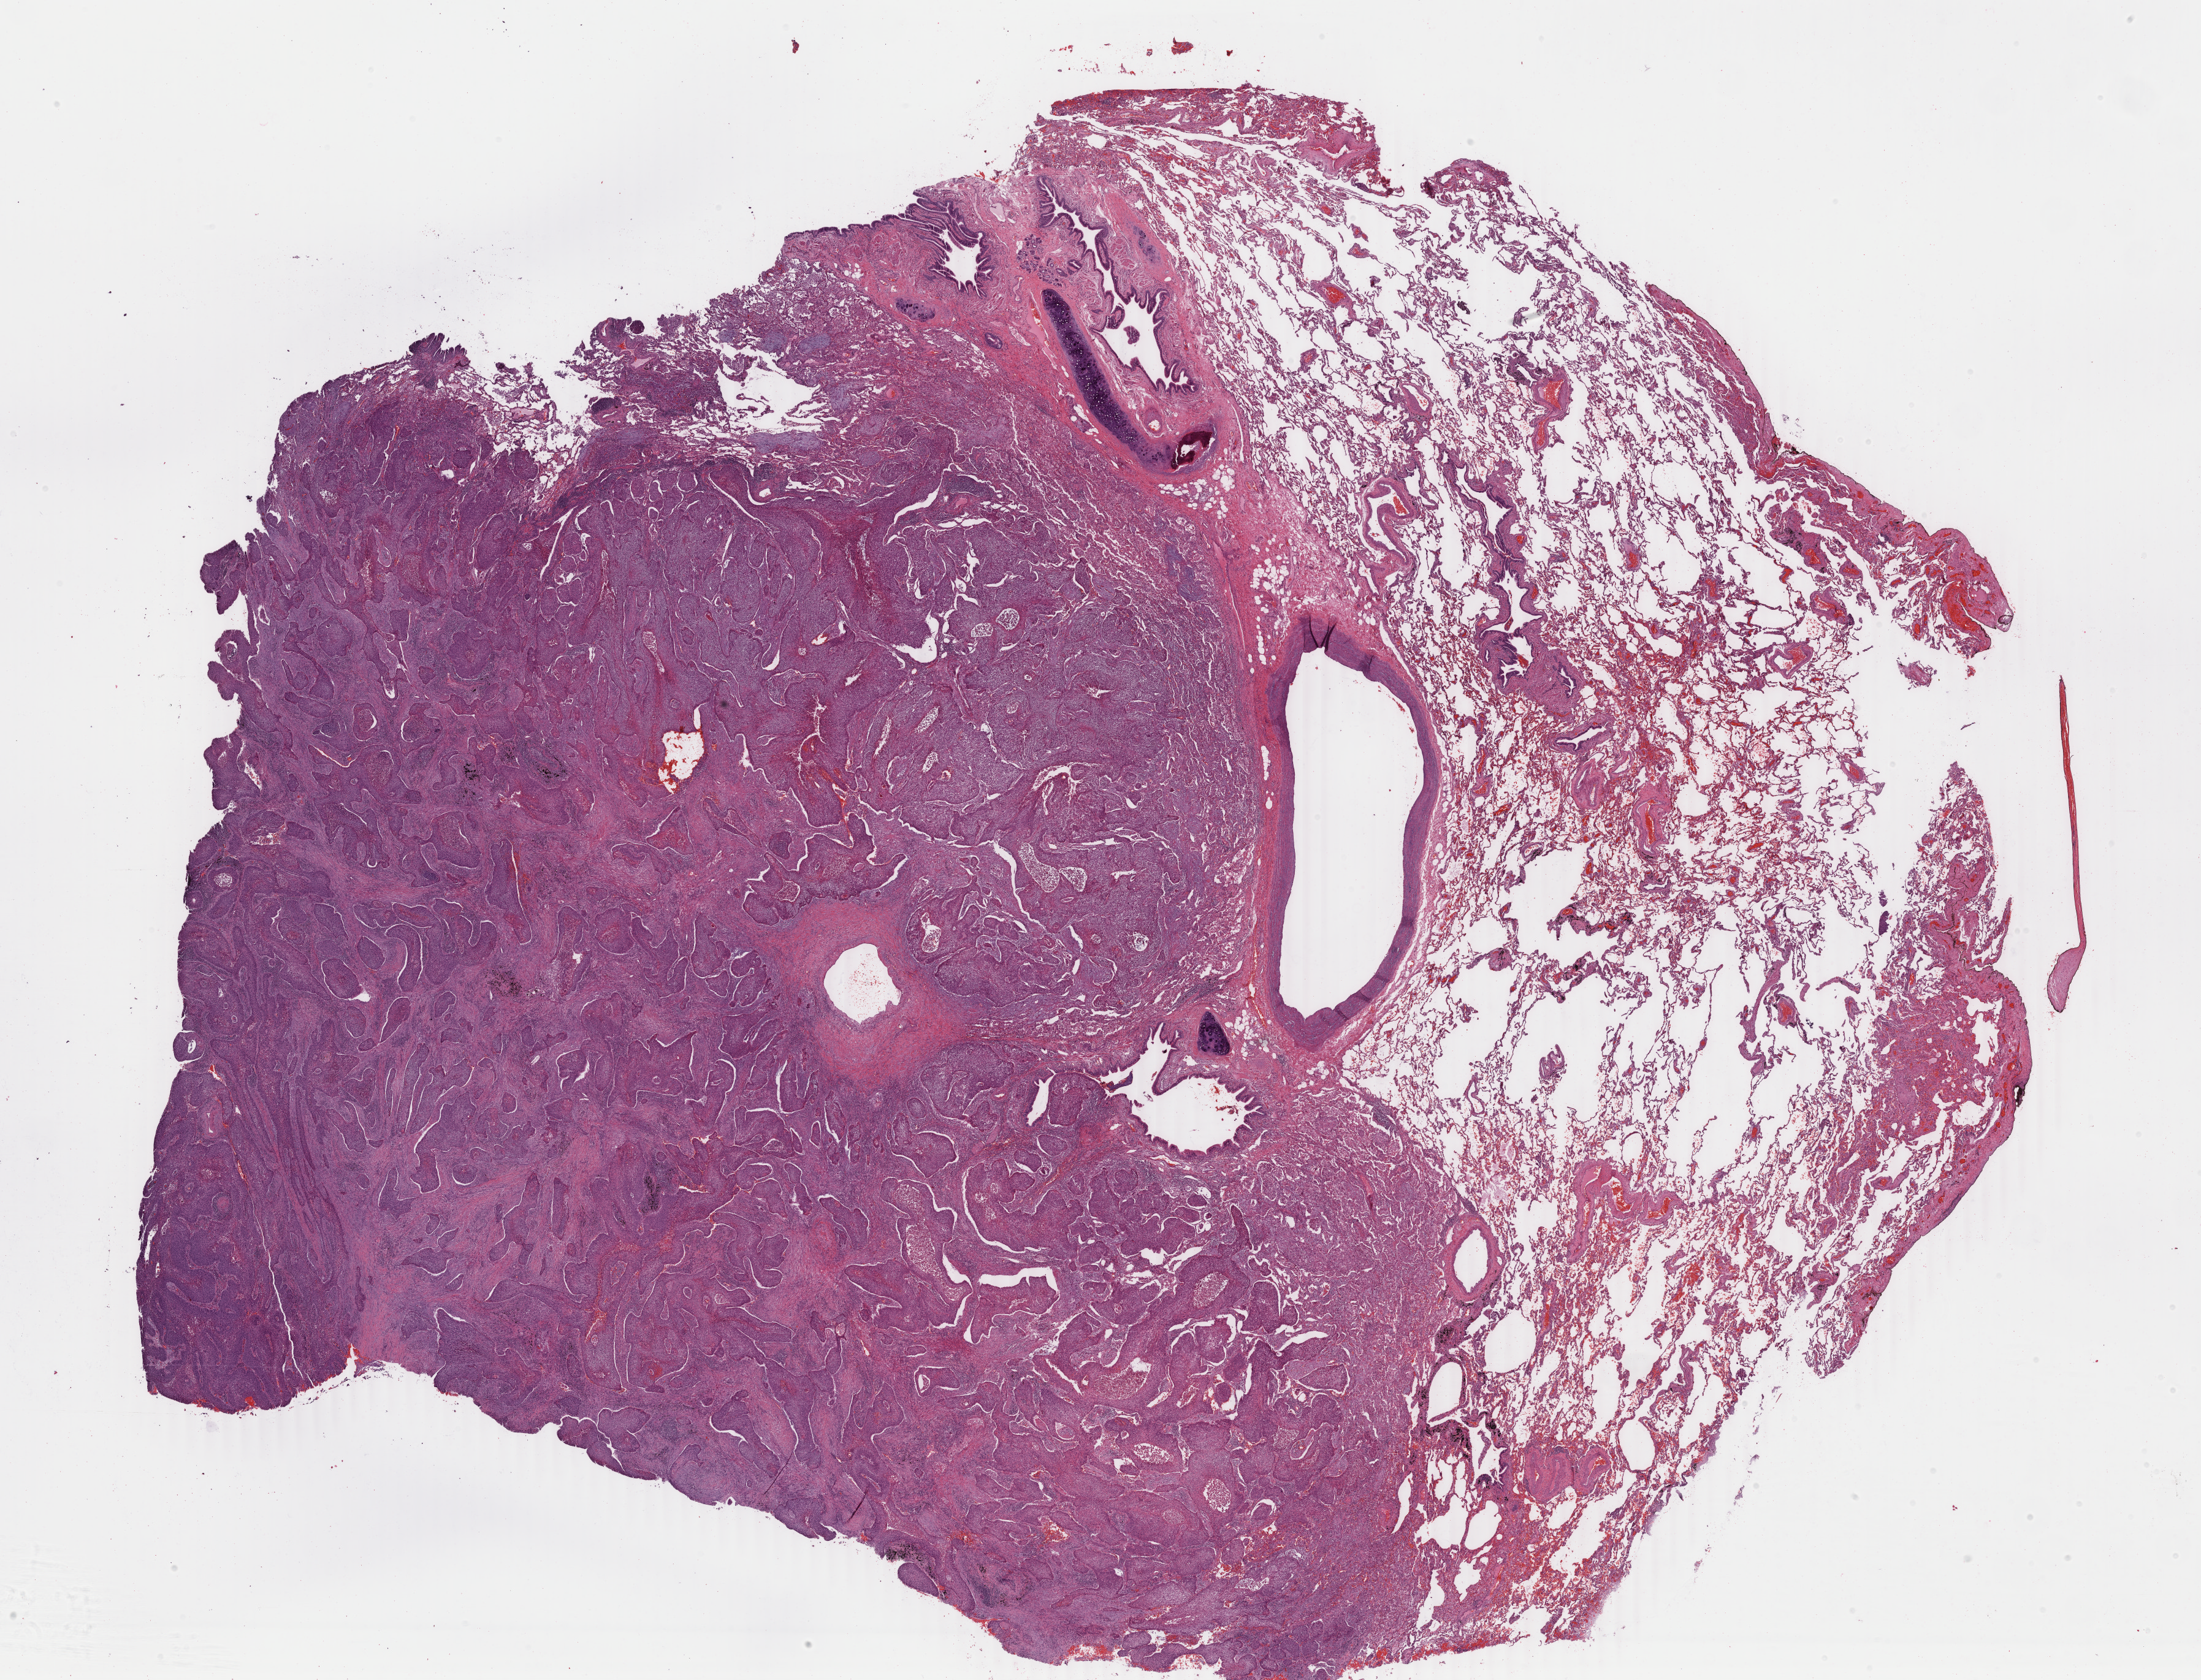
Hematoxylin and eosin (H&E) stained whole-slide image, low-resolution overview of the scanned area, about 28.6 x 21.8 mm; formalin-fixed paraffin-embedded (FFPE) diagnostic section; primary tumour sample from the lung. Patient: male, age at initial diagnosis 83 years.
Diagnosis: Squamous cell carcinoma, NOS (lower lobe, lung).